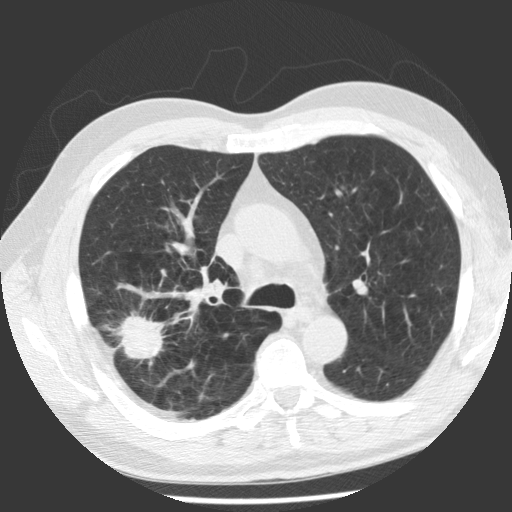
Axial slice from a low-dose chest CT screening exam, baseline screening round, lung window (W 1500 / L -600 HU). Male participant, aged 62 years at enrolment. Former smoker at enrolment.
Expert-annotated lung lesion, bounding box <106,299,180,369> (left, top, right, bottom; pixels). The screening reader recorded 2 non-calcified nodules or masses ≥4 mm on this exam (right upper lobe, right upper lobe); which of them this box marks is not recorded. Official screen result: positive, change unspecified: nodule(s) >= 4 mm or enlarging nodule(s), mass(es), or other non-specific abnormalities suspicious for lung cancer. Later outcome: lung cancer diagnosed 71 days after this screen — adenocarcinoma, NOS, right upper lobe, poorly differentiated (G3), stage IV (AJCC 6th edition), 30 mm at pathology.